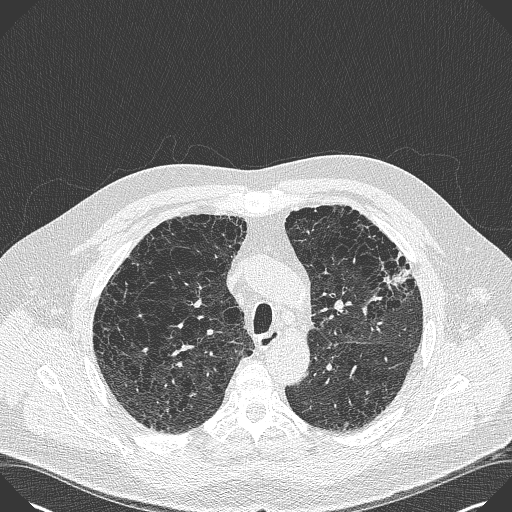
Low-dose screening chest CT, axial slice, baseline screening round, lung window (W 1500 / L -600 HU), slice 117 of 383 in the series, 512 × 512 image matrix. Male participant, aged 59 years at enrolment.
• Expert reader's lesion annotation, bounding box <374,244,428,295> (left, top, right, bottom; pixels).
• Screening reader's record for this exam: no non-calcified nodule ≥4 mm recorded.
• Official screen result: negative screen, minor abnormalities not suspicious for lung cancer.
• Lung cancer was diagnosed 909 days after this screen: bronchiolo-alveolar carcinoma, mixed mucinous and non-mucinous, left upper lobe, stage IA (AJCC 6th edition), 20 mm at pathology.